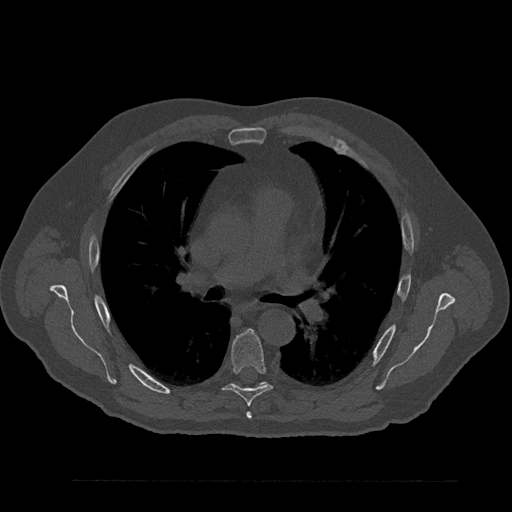
CT including the spine, one axial slice. Reconstruction kernel Br40s/3. 120 kVp. Bone window (W 1800 / L 400 HU). 0.5 mm slice thickness. 512 × 512 image matrix, field of view 430 × 430 mm. Male patient, age 61 years. Case-level facts recorded for this patient, not image findings: primary cancer: prostate.
Outlined on this slice (semi-automatically segmented with operator editing):
- T5 vertebra: bounding box [x1, y1, x2, y2] px = [246, 412, 252, 419]
- T6 vertebra: [222, 330, 272, 406]
- T7 vertebra: [237, 382, 267, 386]